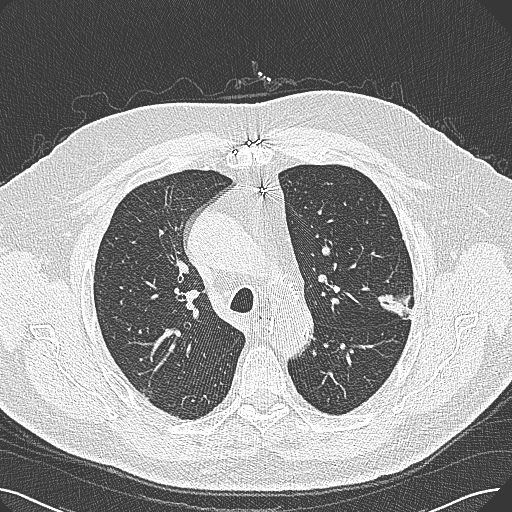
Chest CT (low-dose screening protocol), one axial image; baseline annual screen; lung window (W 1500 / L -600 HU); 1 mm slice thickness; 512 × 512 image matrix. Male, age 74 years at enrolment. Former smoker at enrolment.
Expert reader's lesion annotation, bounding box (x1, y1, x2, y2) in pixels: (368, 273, 425, 323). The exam's reader record, not a measurement of the box and not confirmed to be the same lesion: non-calcified nodule or mass ≥4 mm, left upper lobe, 15 × 10 mm, poorly defined margins, soft tissue attenuation. Later outcome: lung cancer diagnosed 124 days after this screen — adenocarcinoma, NOS, left upper lobe, well differentiated (G1), stage IA (AJCC 6th edition), 26 mm at pathology.